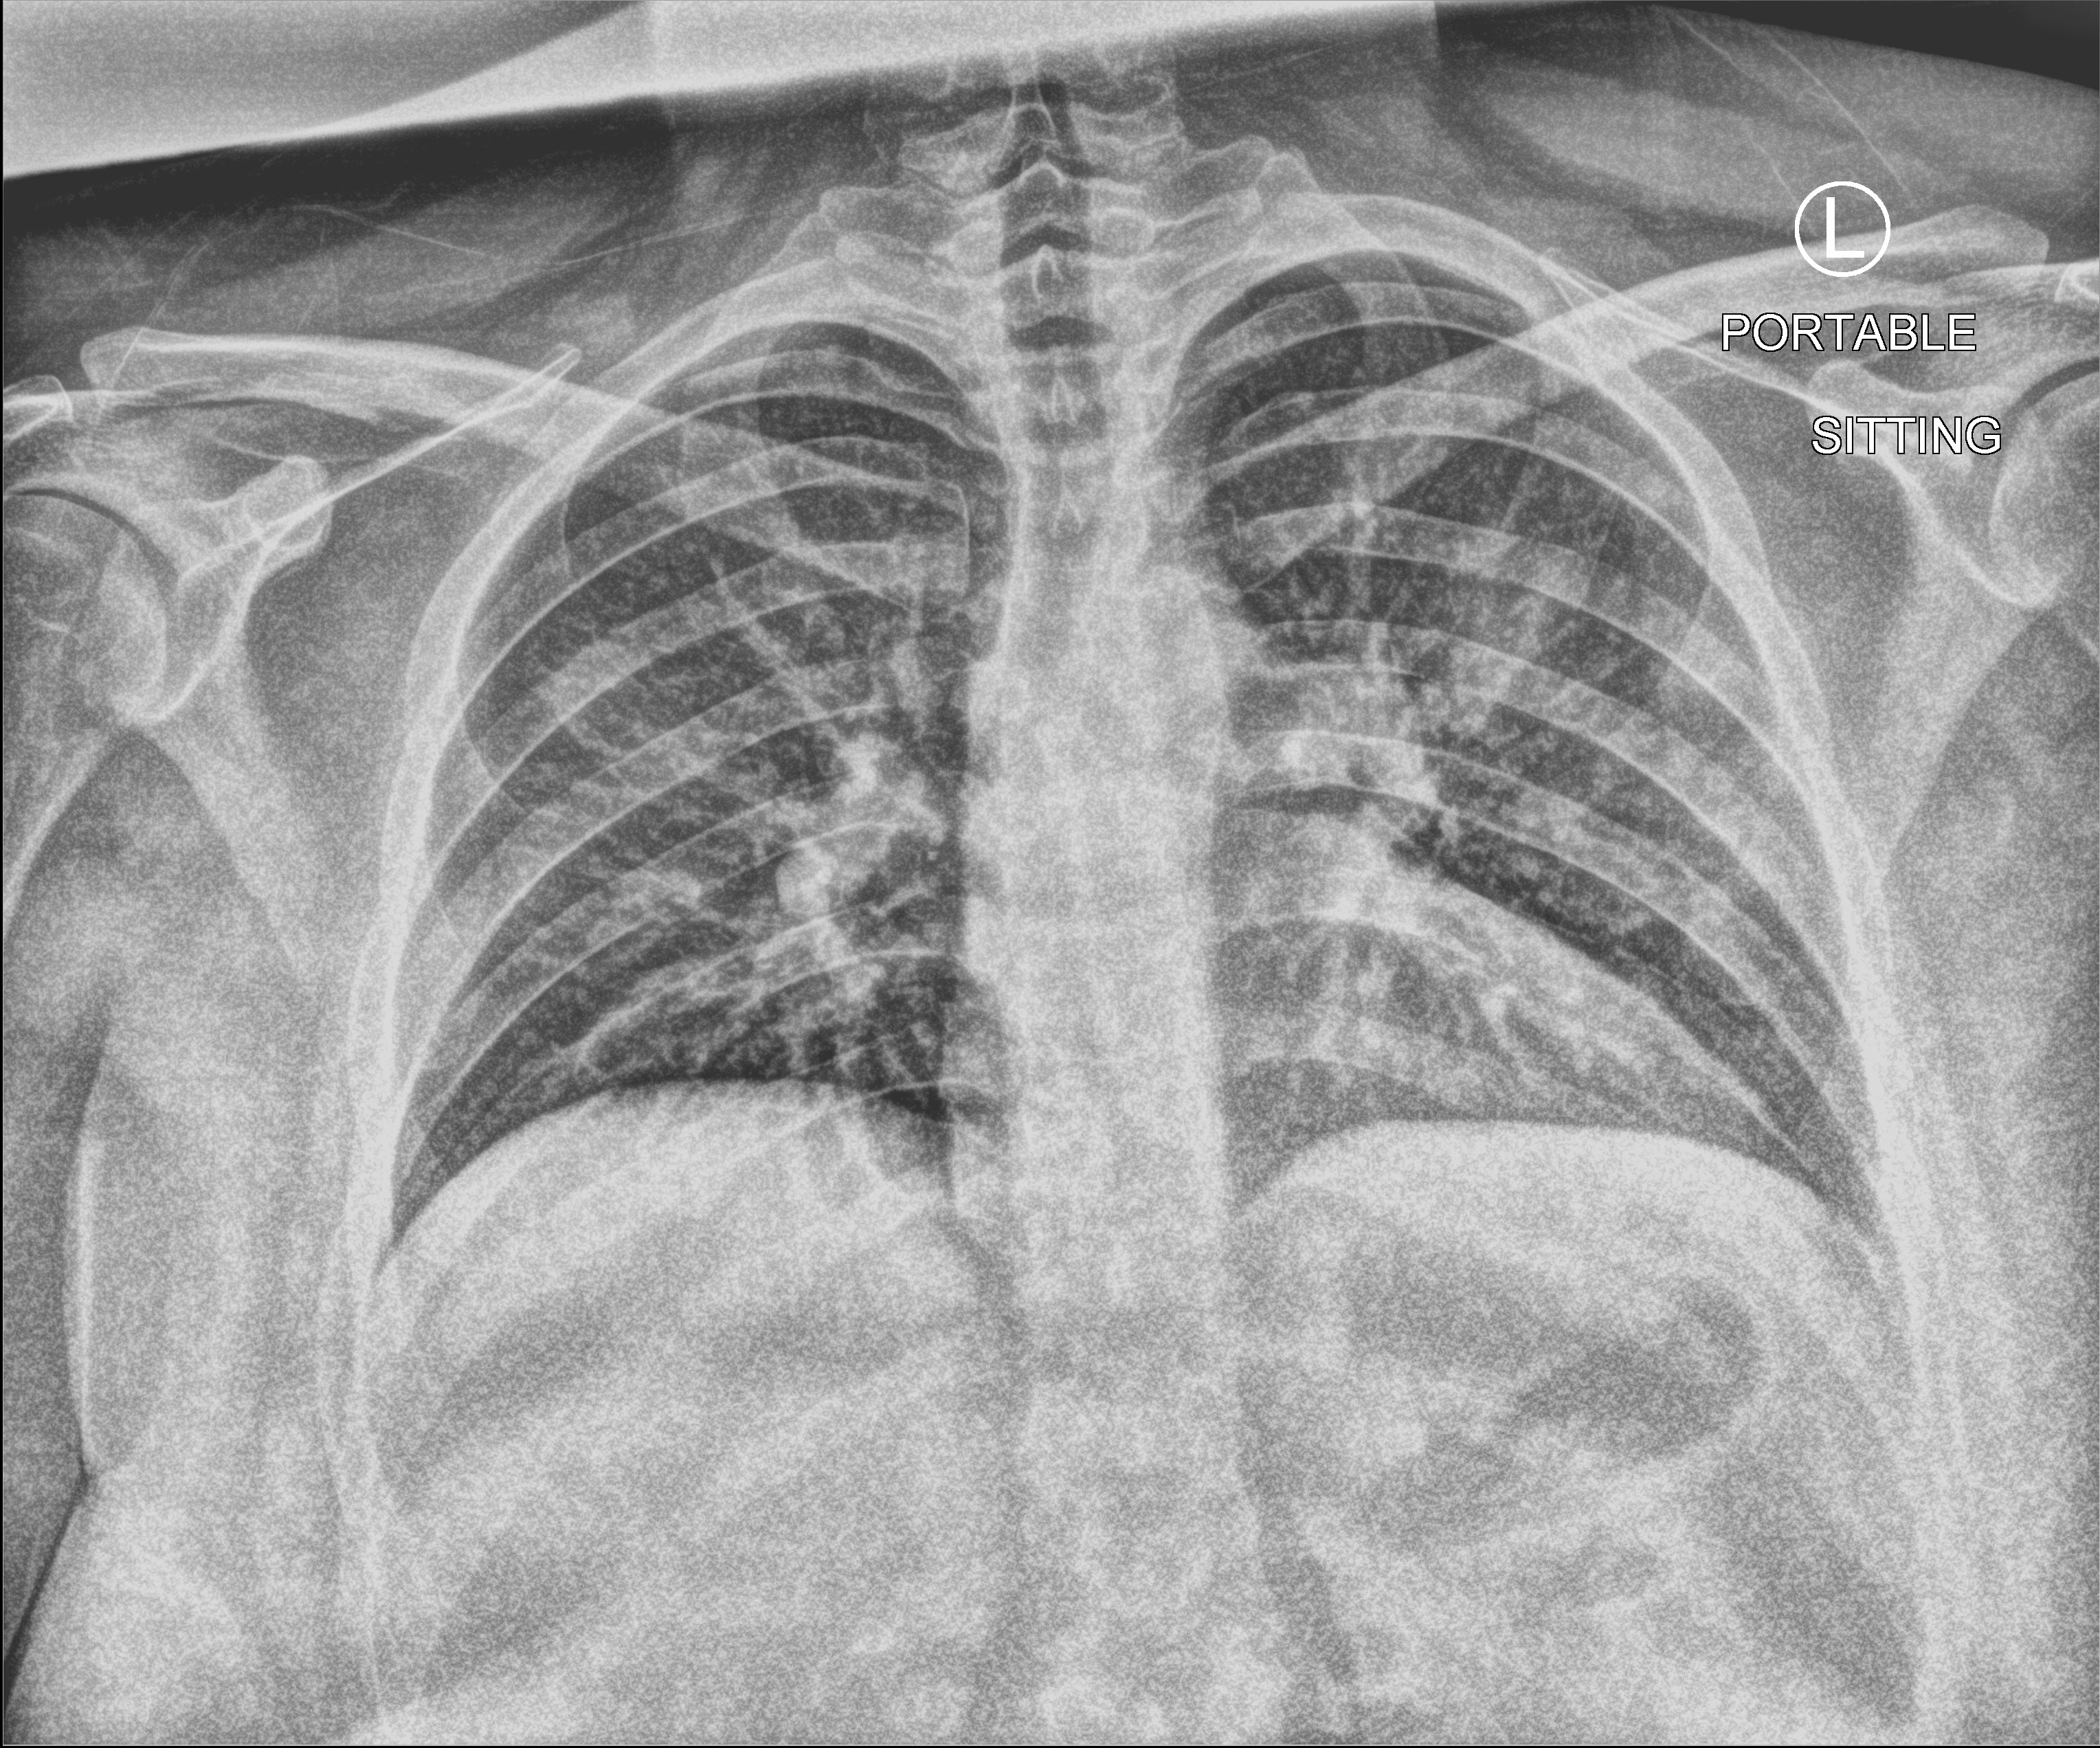
Chest X-ray (portable). Female patient hospitalised with COVID-19, age 18–59 years.
Hospital-stay facts (about this admission, not read from this image; timing relative to this image not recorded): mechanically ventilated during this hospital stay: no.